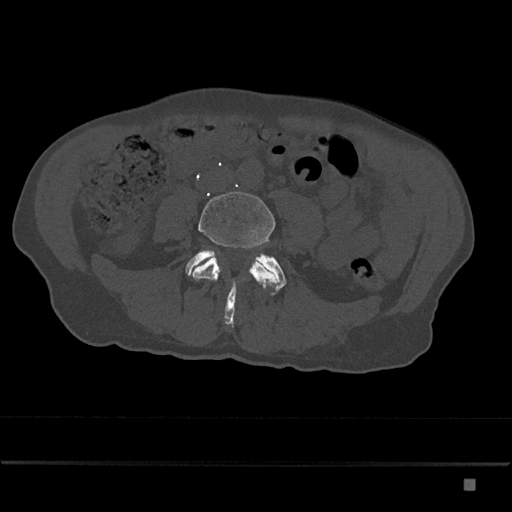
CT including the spine, one axial slice; reconstruction kernel Br40s/3; 120 kVp; bone window (W 1800 / L 400 HU); 512 × 512 image matrix, field of view 390 × 390 mm. Patient: male, 72 years. From the clinical record (not read from this slice): primary cancer: prostate.
Outlined on this slice (semi-automatic segmentation, software-assisted and operator-edited):
- L4 vertebra: box from (x=190, y=191) to (x=277, y=305) px
- L5 vertebra: (x=185, y=250)–(x=286, y=325)